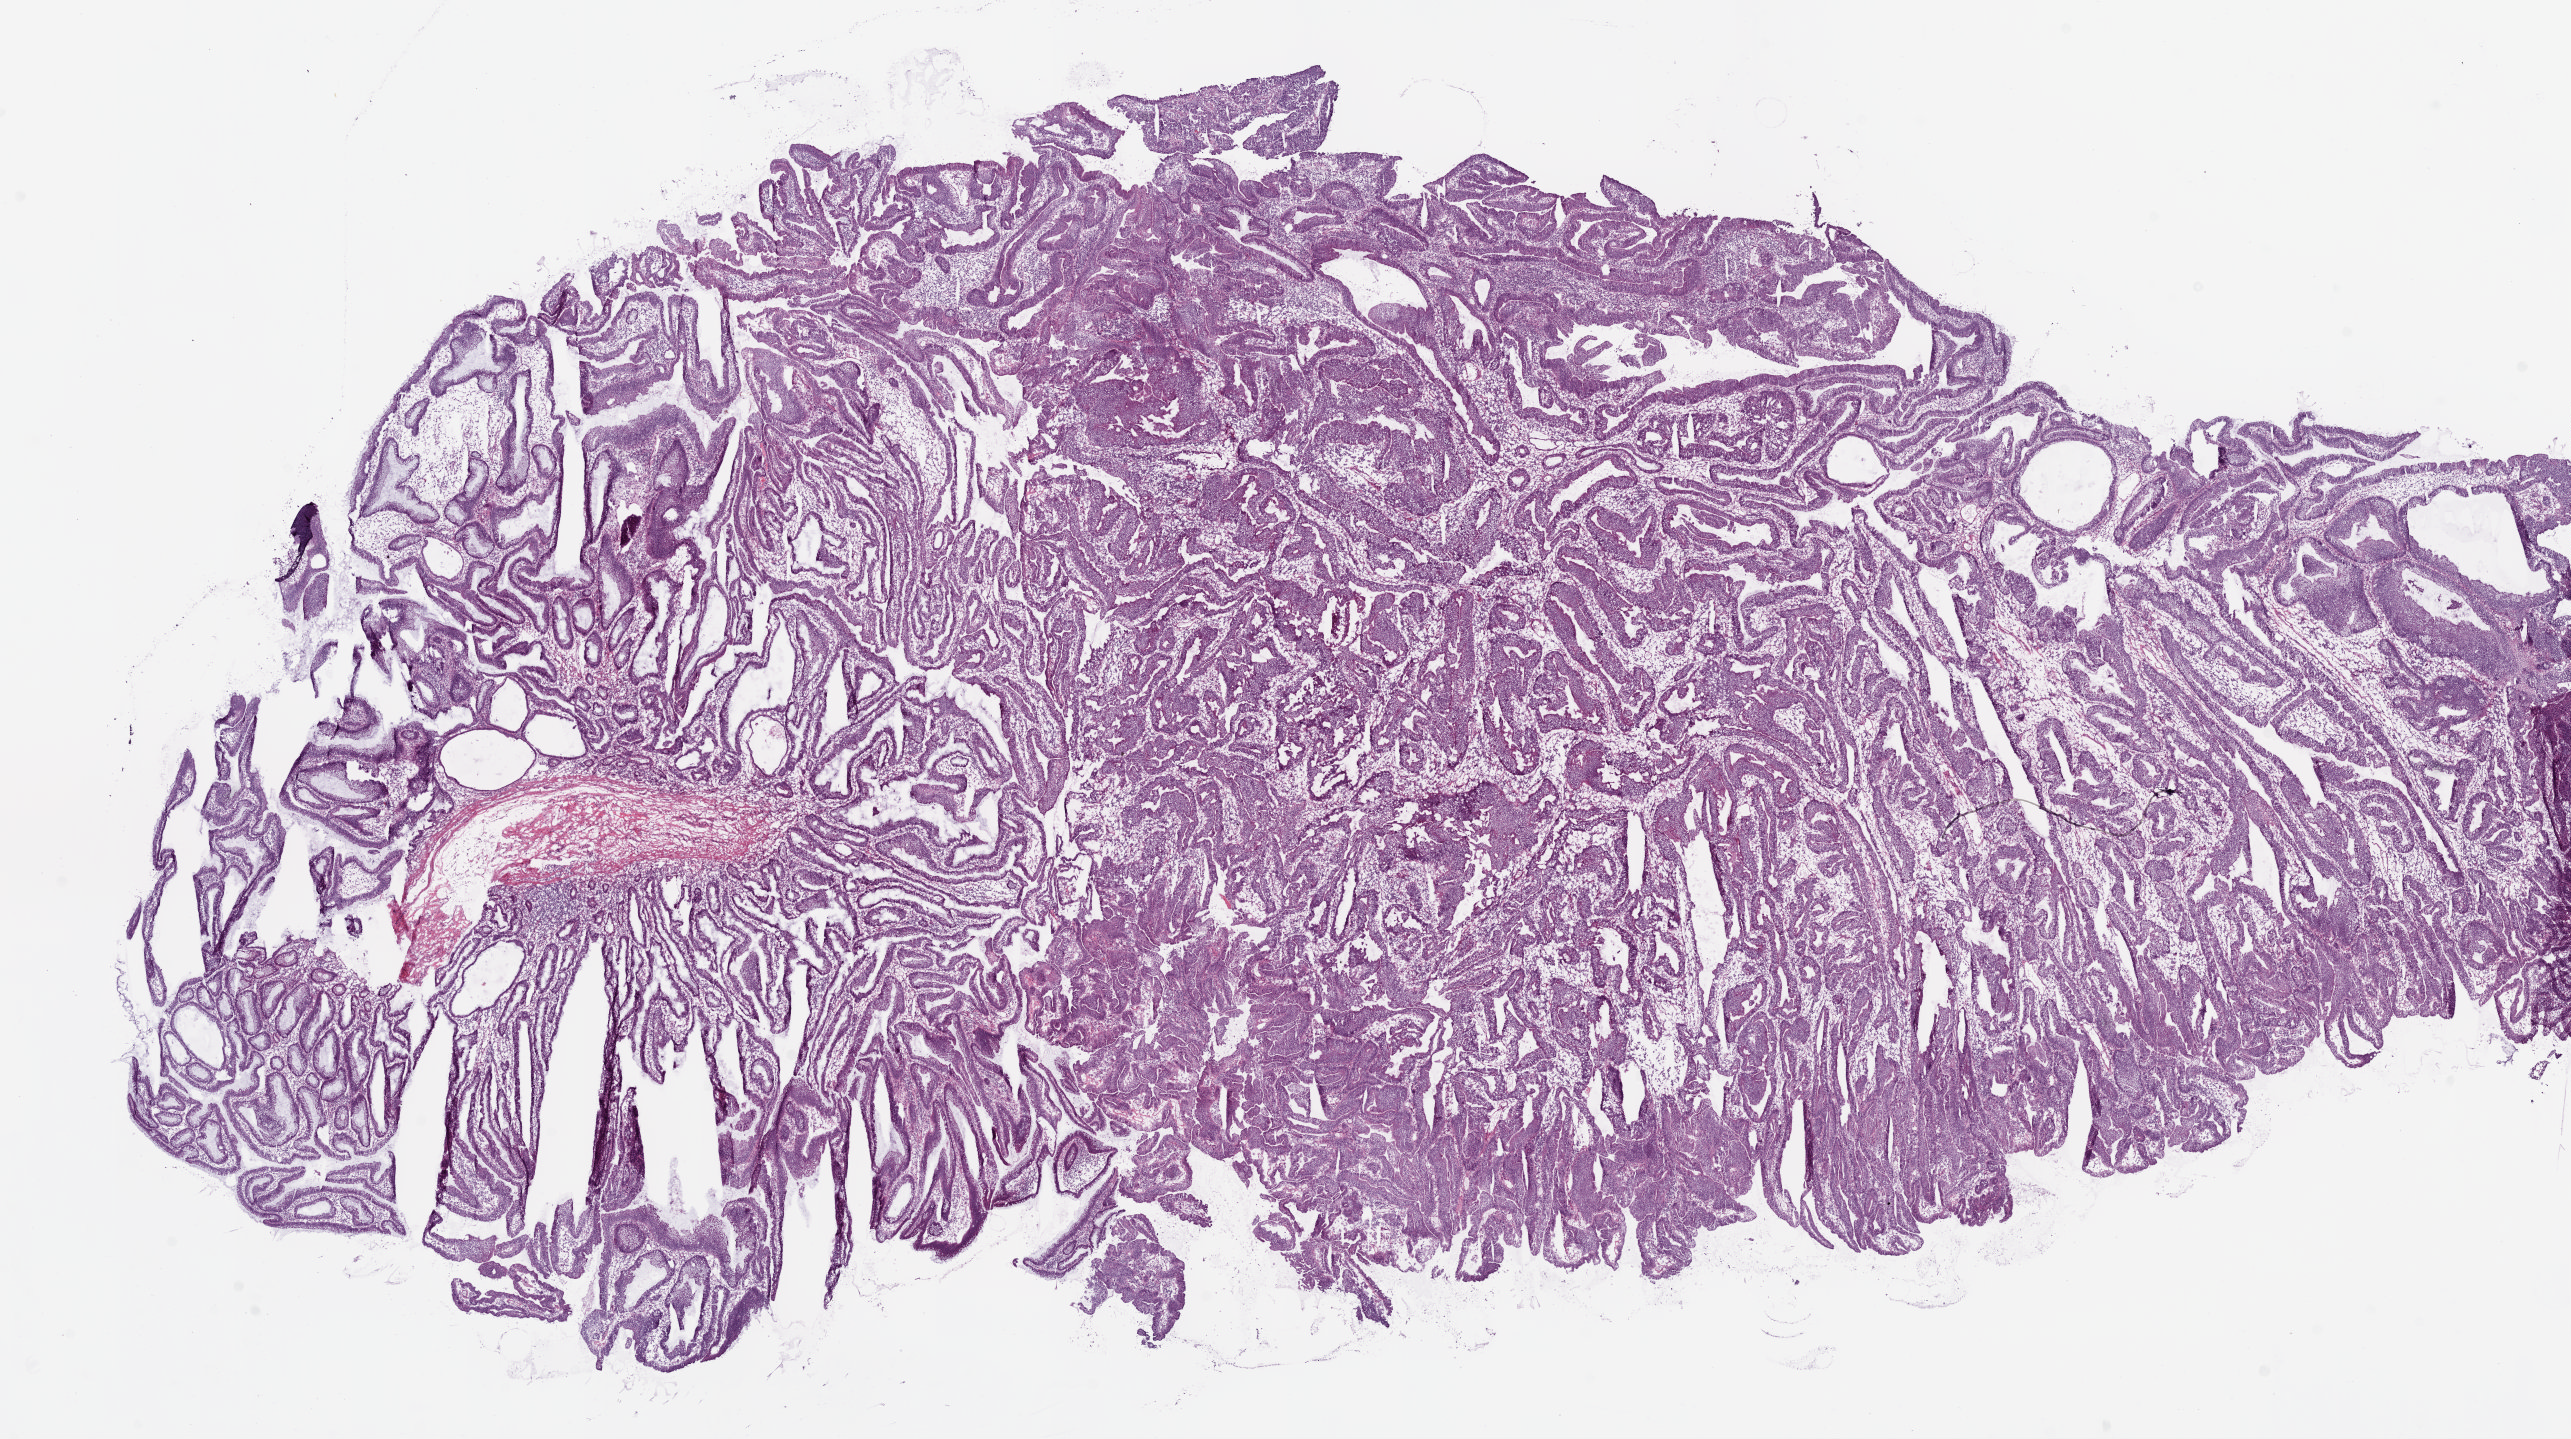
Whole-slide histology image, H&E, shown as a low-resolution overview of the whole scanned area (about 20.6 x 11.5 mm), frozen section from the top of the tissue portion, primary tumour sample from the colon. Patient: female, age at initial diagnosis 51 years. Pathologist review of this section (percent, as recorded): tumour cells 75%, tumour nuclei 75%, normal cells 15%, stromal cells 10%, necrosis 0%.
Histologic diagnosis: Adenocarcinoma, NOS (cecum). Lymph nodes positive (case pathology): 0 of 16 examined. AJCC pathologic stage: I (6th edition).